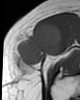
MRI of an extremity soft-tissue mass, one axial slice. Position 19 of 46 along the scan axis. MR volume resampled by the dataset authors to the PET/CT grid (not the native acquisition matrix). 3.27 mm slice thickness. 80 × 100 image matrix, field of view 78 × 98 mm. Female patient. From the clinical record (not read from this slice): histological type: synovial sarcoma; grade: intermediate; site of the primary tumour: right thigh.
Outlined on this slice (expert contour drawn on MRI and transferred to this co-registered scan by the dataset authors):
- gross tumour volume including surrounding oedema: bounding box [x1, y1, x2, y2] px = [12, 21, 63, 70]
- gross tumour volume (mass): [12, 21, 63, 70]